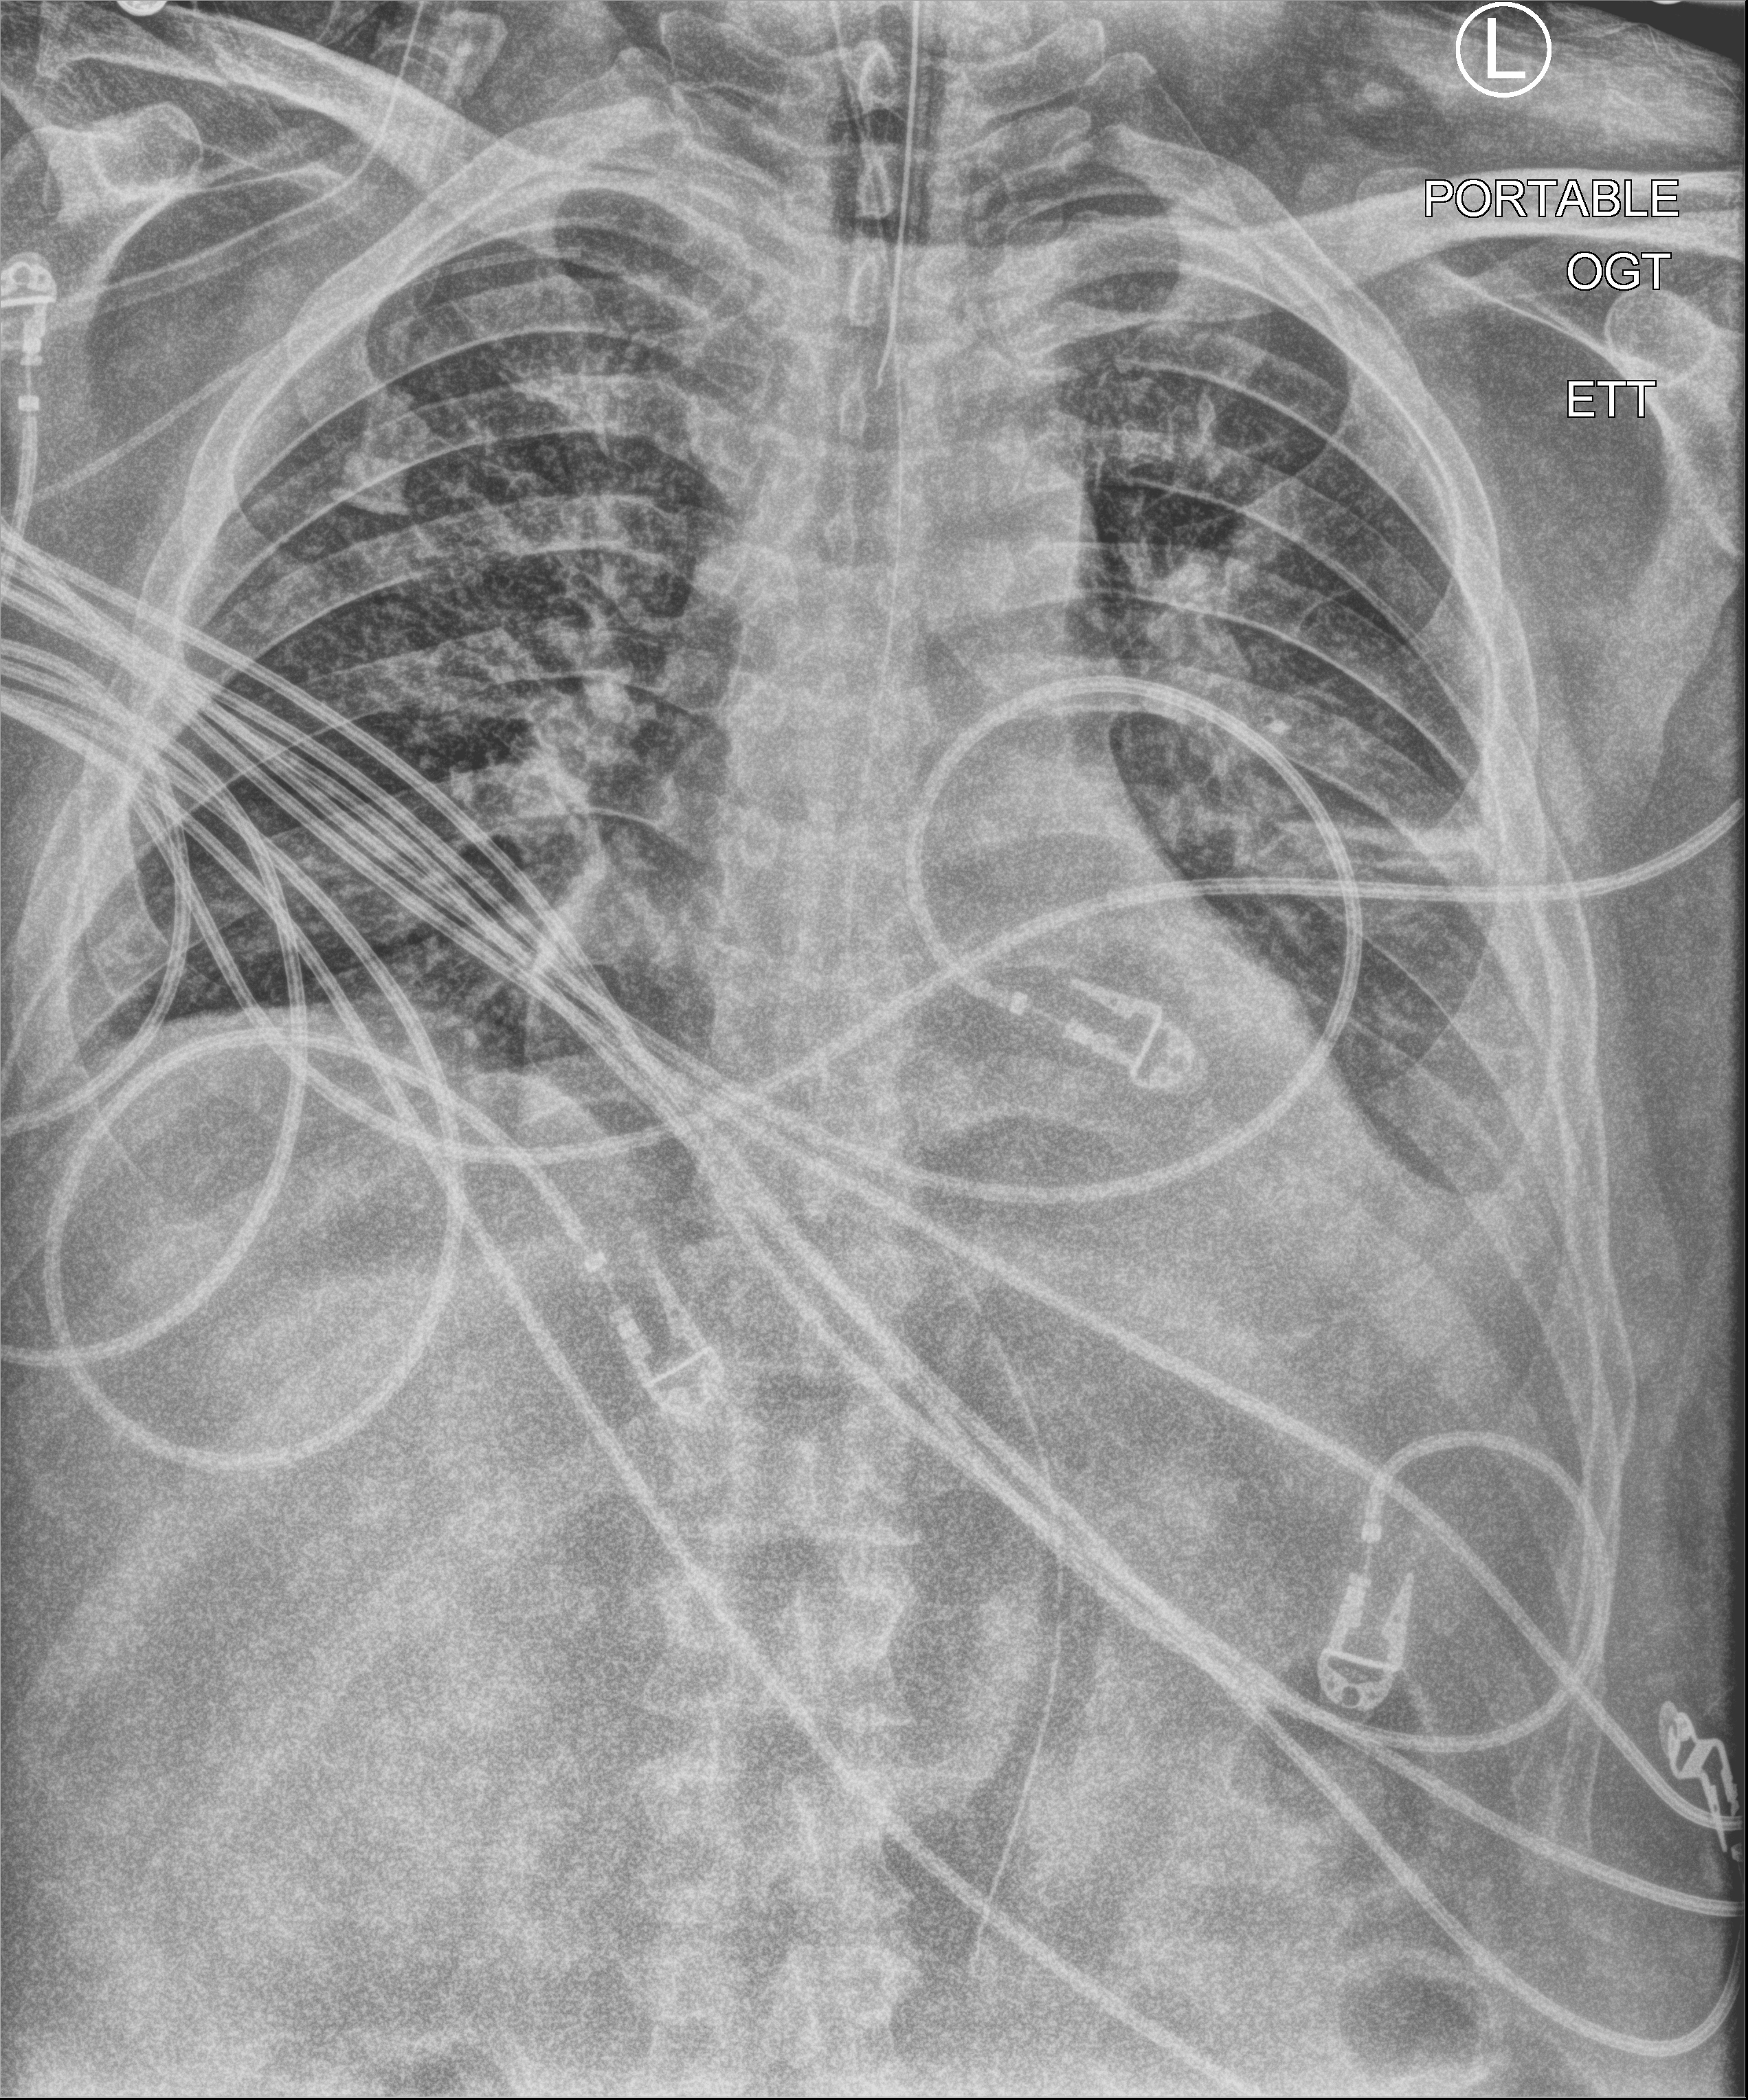
Chest X-ray (portable); anteroposterior (AP) projection. Patient hospitalised with COVID-19; male, aged 18–59 years.
Admission-level facts for this patient (not findings on this image; timing relative to this image not recorded): admitted to intensive care during this hospital stay: yes.